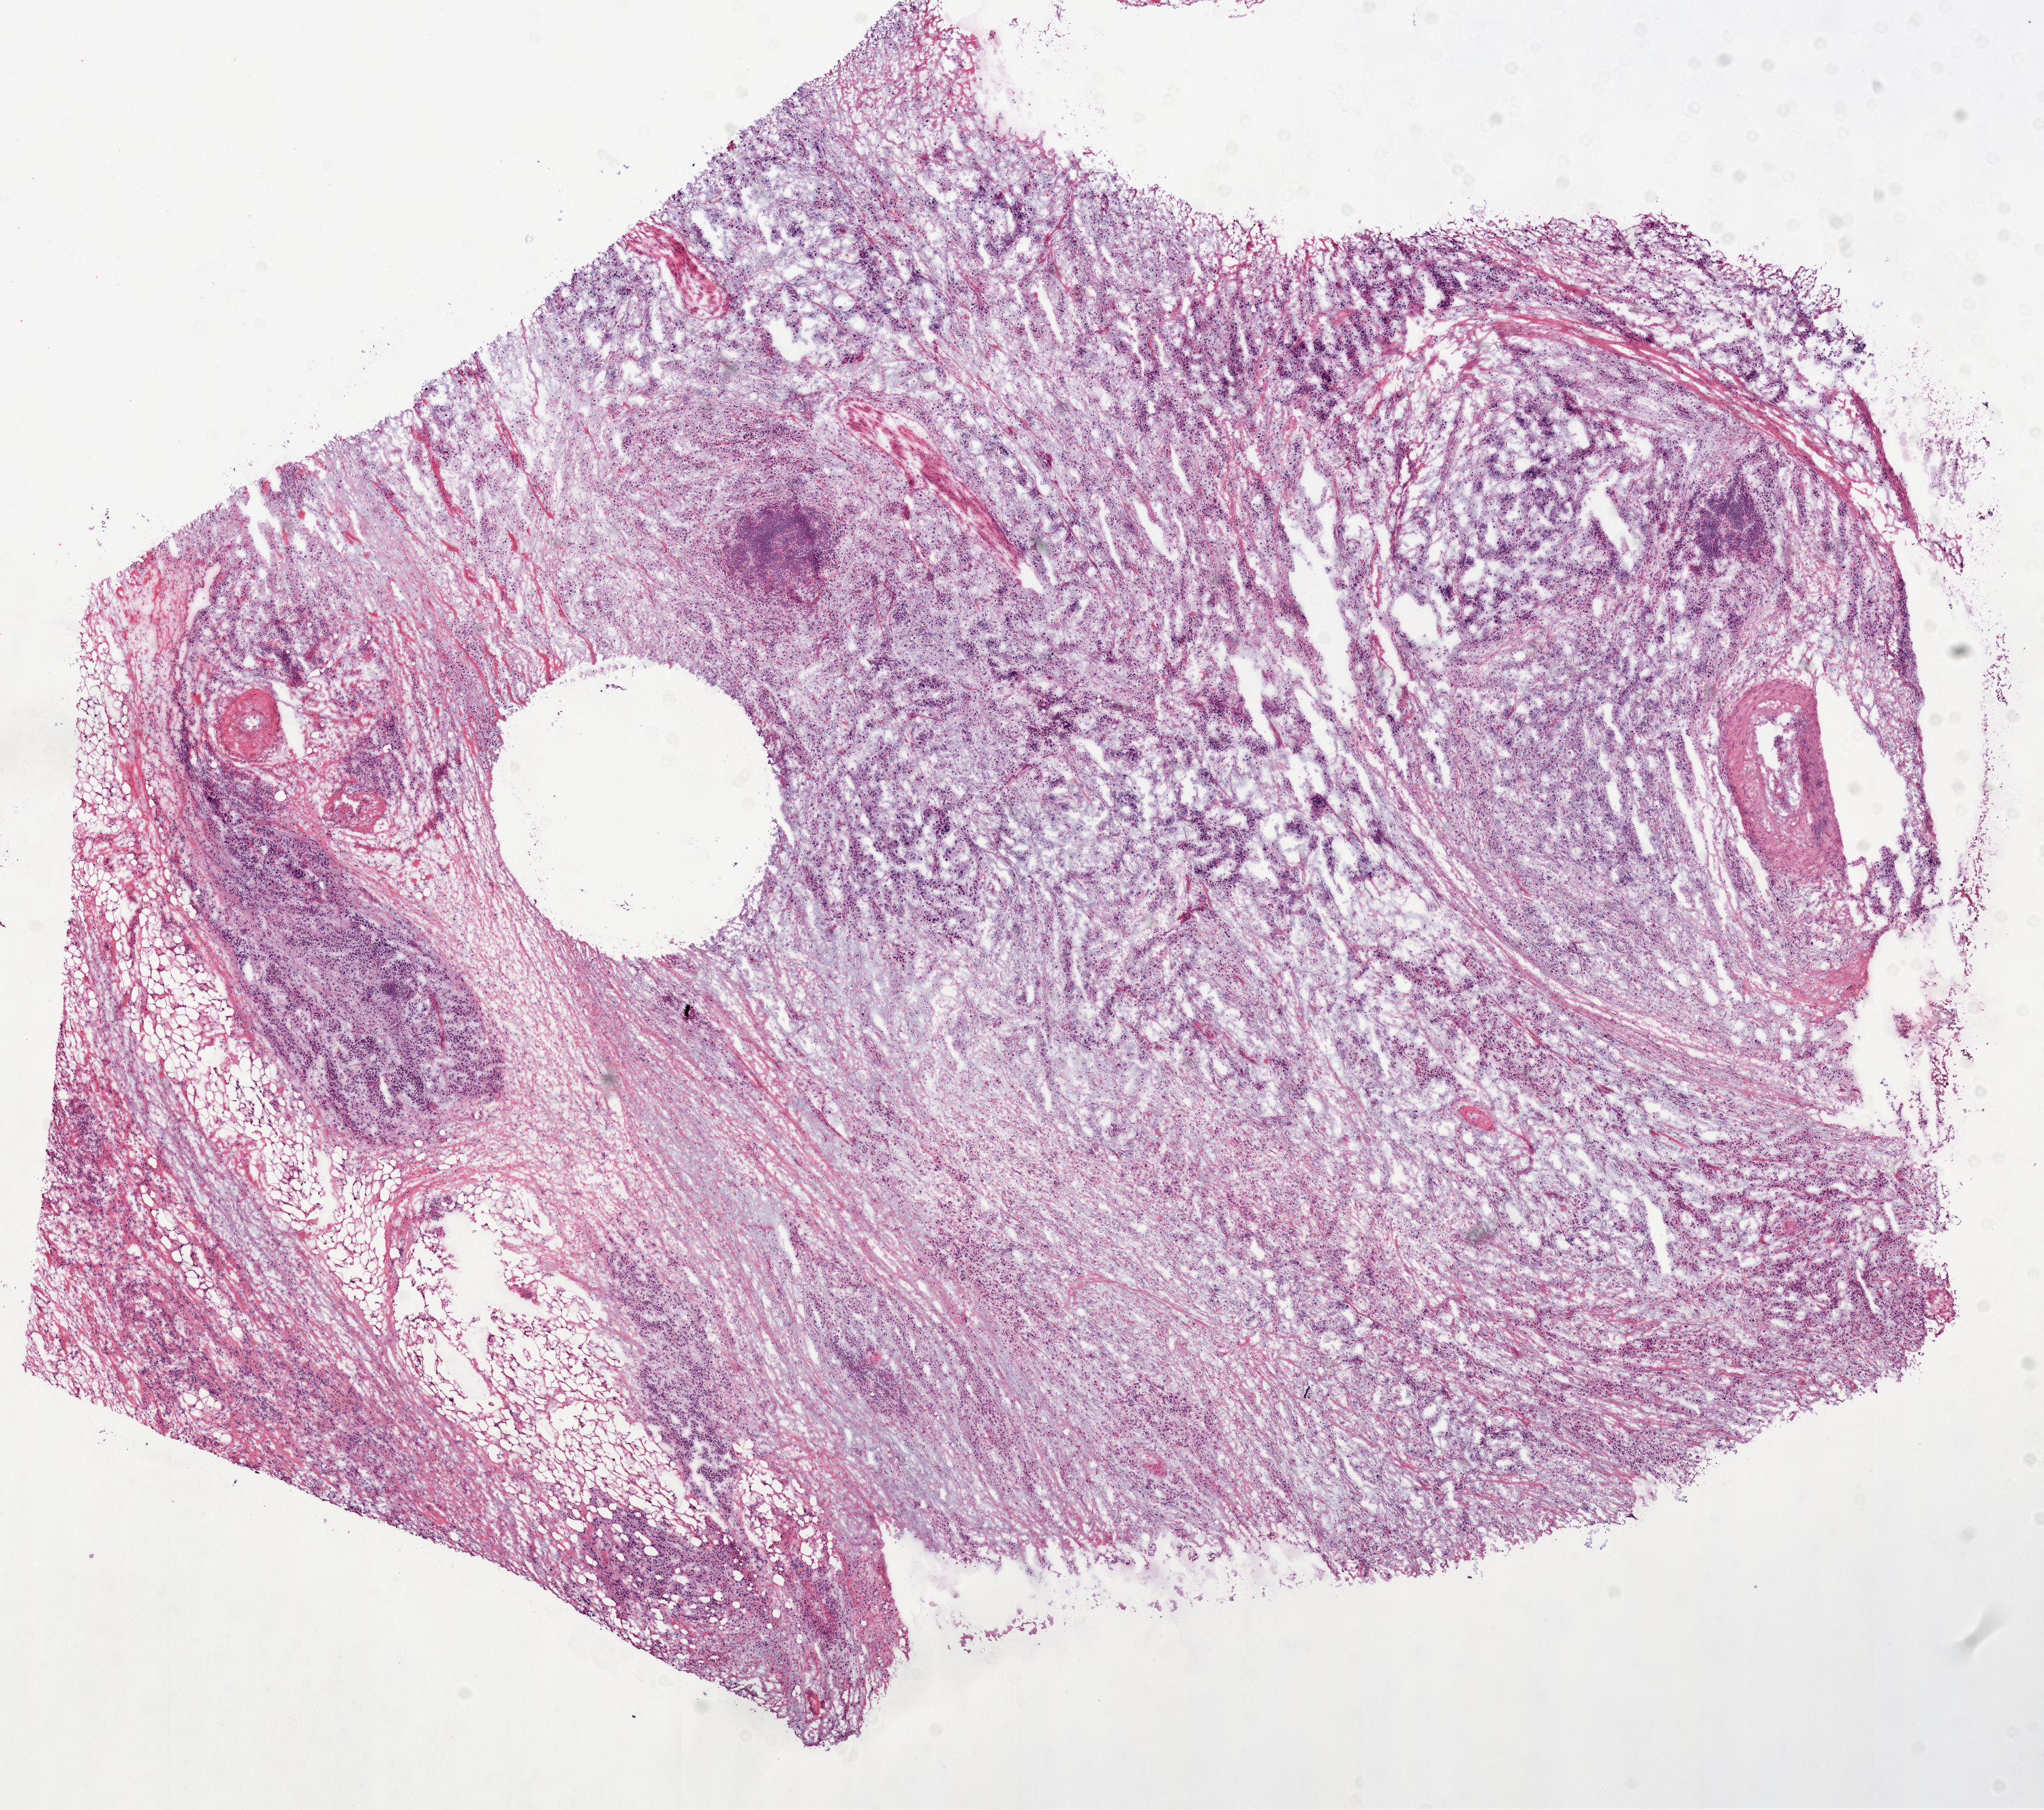
H&E whole-slide image, a low-resolution overview of the entire scanned area, about 12.0 x 10.7 mm, frozen section from the top of the tissue portion, primary tumour sample from the stomach. Male patient; age at initial diagnosis 60 years. Histologic grade: G3 (poorly differentiated). Pathologist review of this section (percent, as recorded): tumour cells 80%, tumour nuclei 75%, normal cells 0%, stromal cells 20%, necrosis 0%.
• AJCC pathologic stage: II (6th edition)
• diagnosis: Mucinous adenocarcinoma (body of stomach)